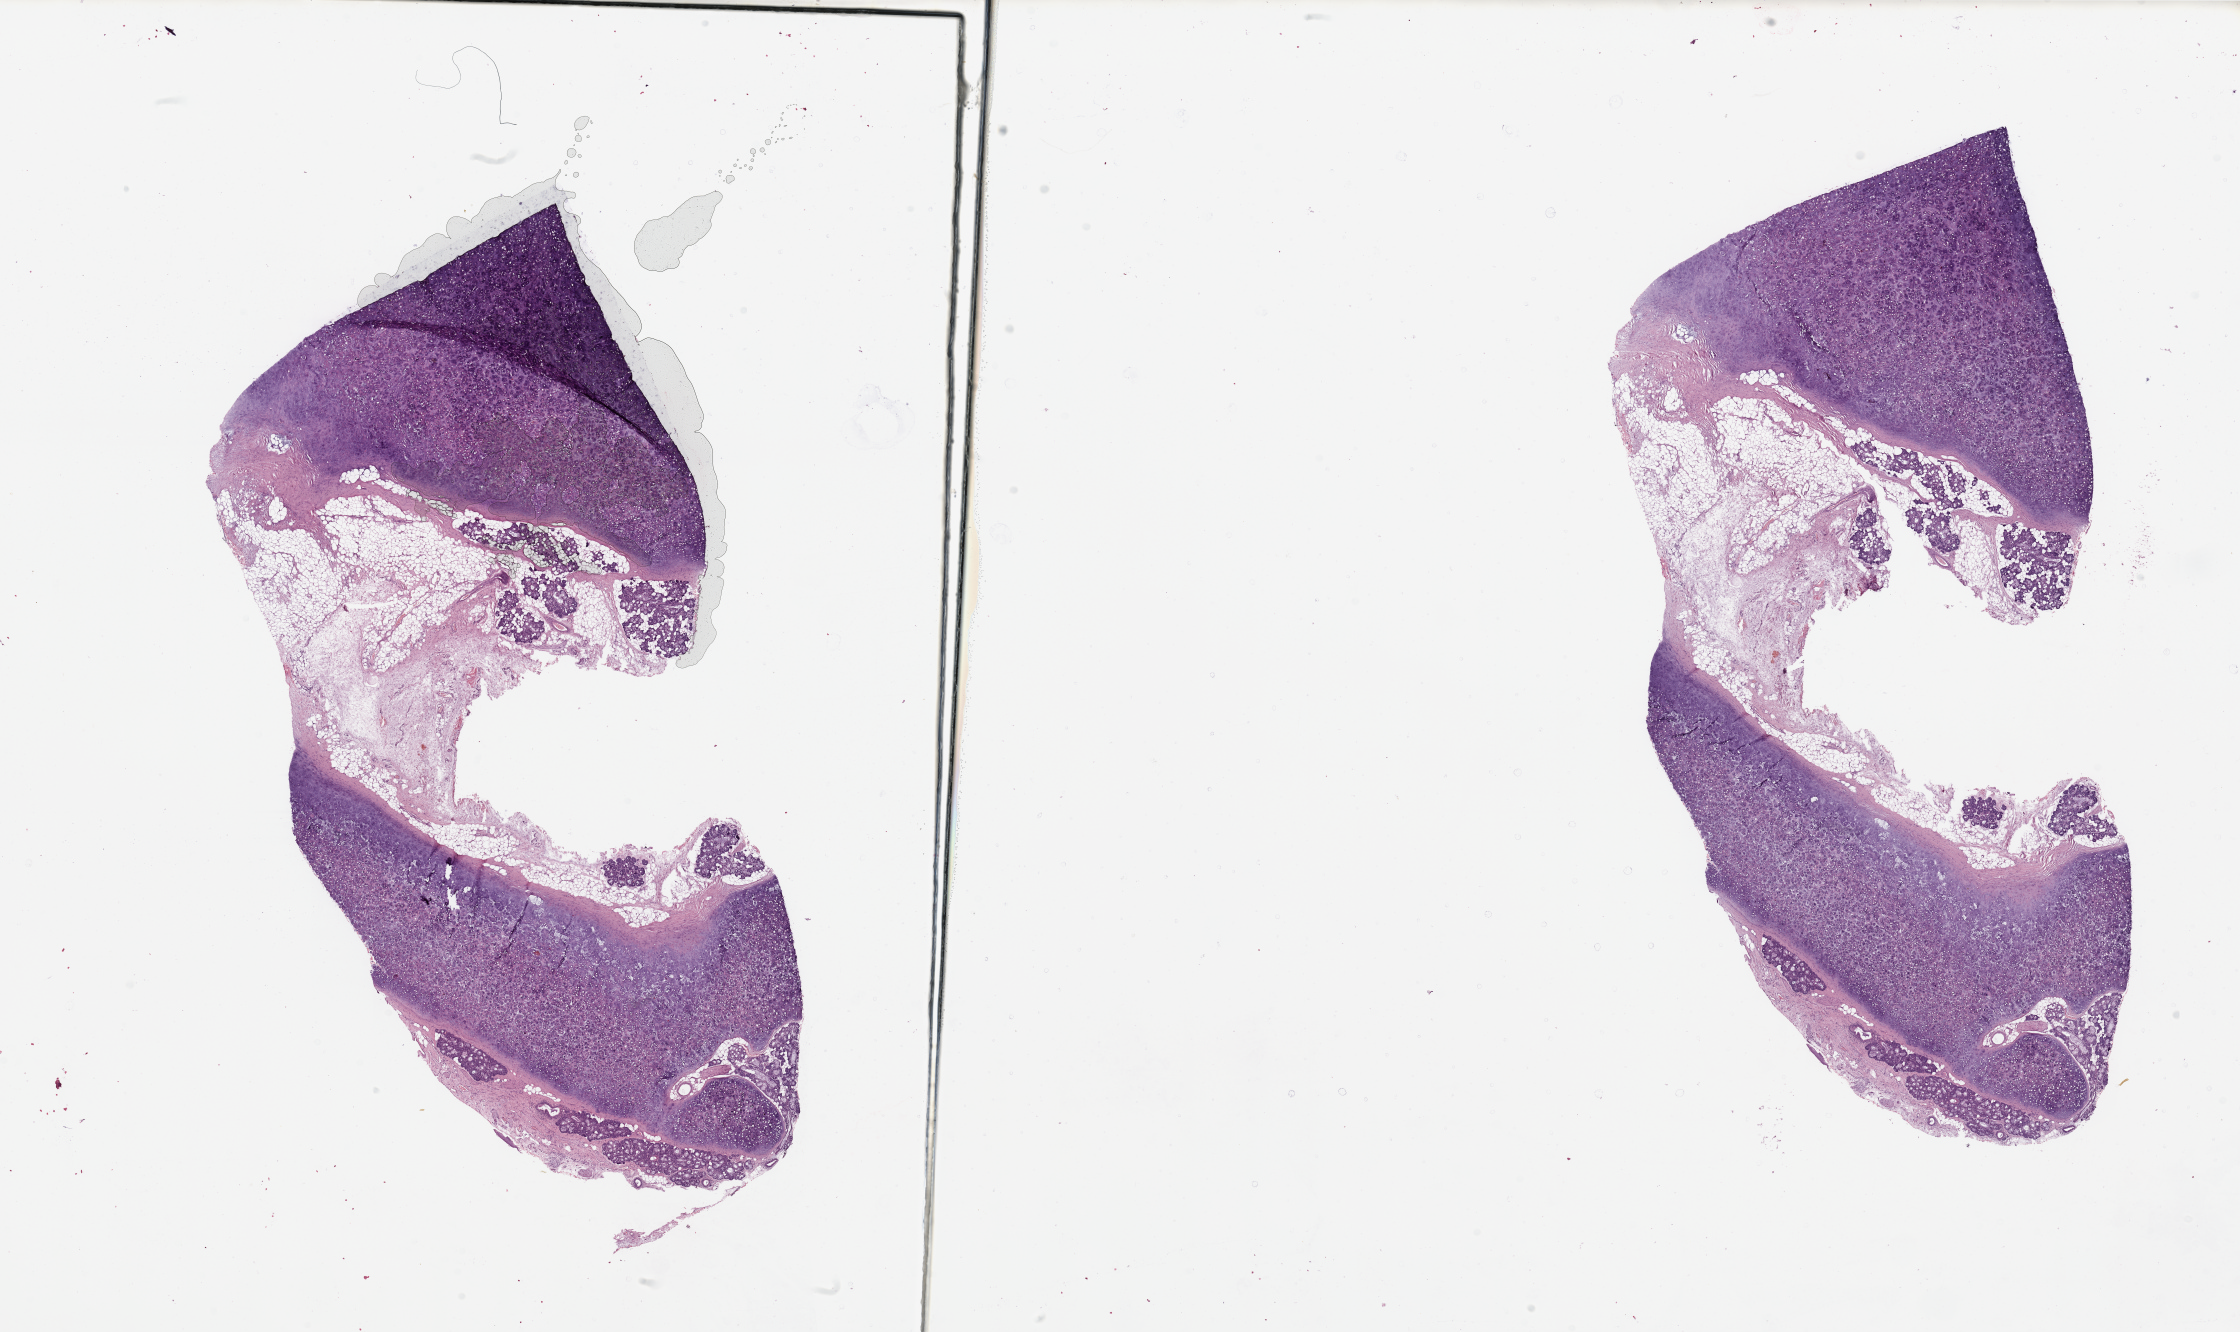
Hematoxylin and eosin (H&E) stained whole-slide image — low-resolution overview of the scanned area, about 35.4 x 21.1 mm (acquisition: 20x scan); normal (non-tumour) tissue sample, sampled site: larynx. 49-year-old male patient.
This section: normal (non-tumour) tissue from the same patient. Patient diagnosis: Squamous cell carcinoma, NOS.